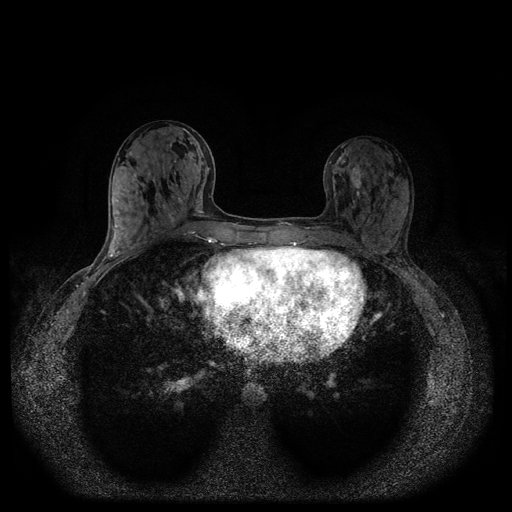
Breast MRI (dynamic contrast-enhanced, multi-phase), one axial slice; slice 42 of 116 in the series (ordered by position); dynamic contrast-enhanced series, time point 2 of 5 at this slice position (early post-contrast); 1.5 T; TE 2.6 ms, TR 5.4 ms; 512 × 512 image matrix, field of view 340 × 340 mm. Patient: female, 32 years.
Outlined on this slice (semi-automatically segmented with operator editing):
- breast lesion (labelled benign in the annotation): bounding box <350,165,364,189> (left, top, right, bottom; pixels)